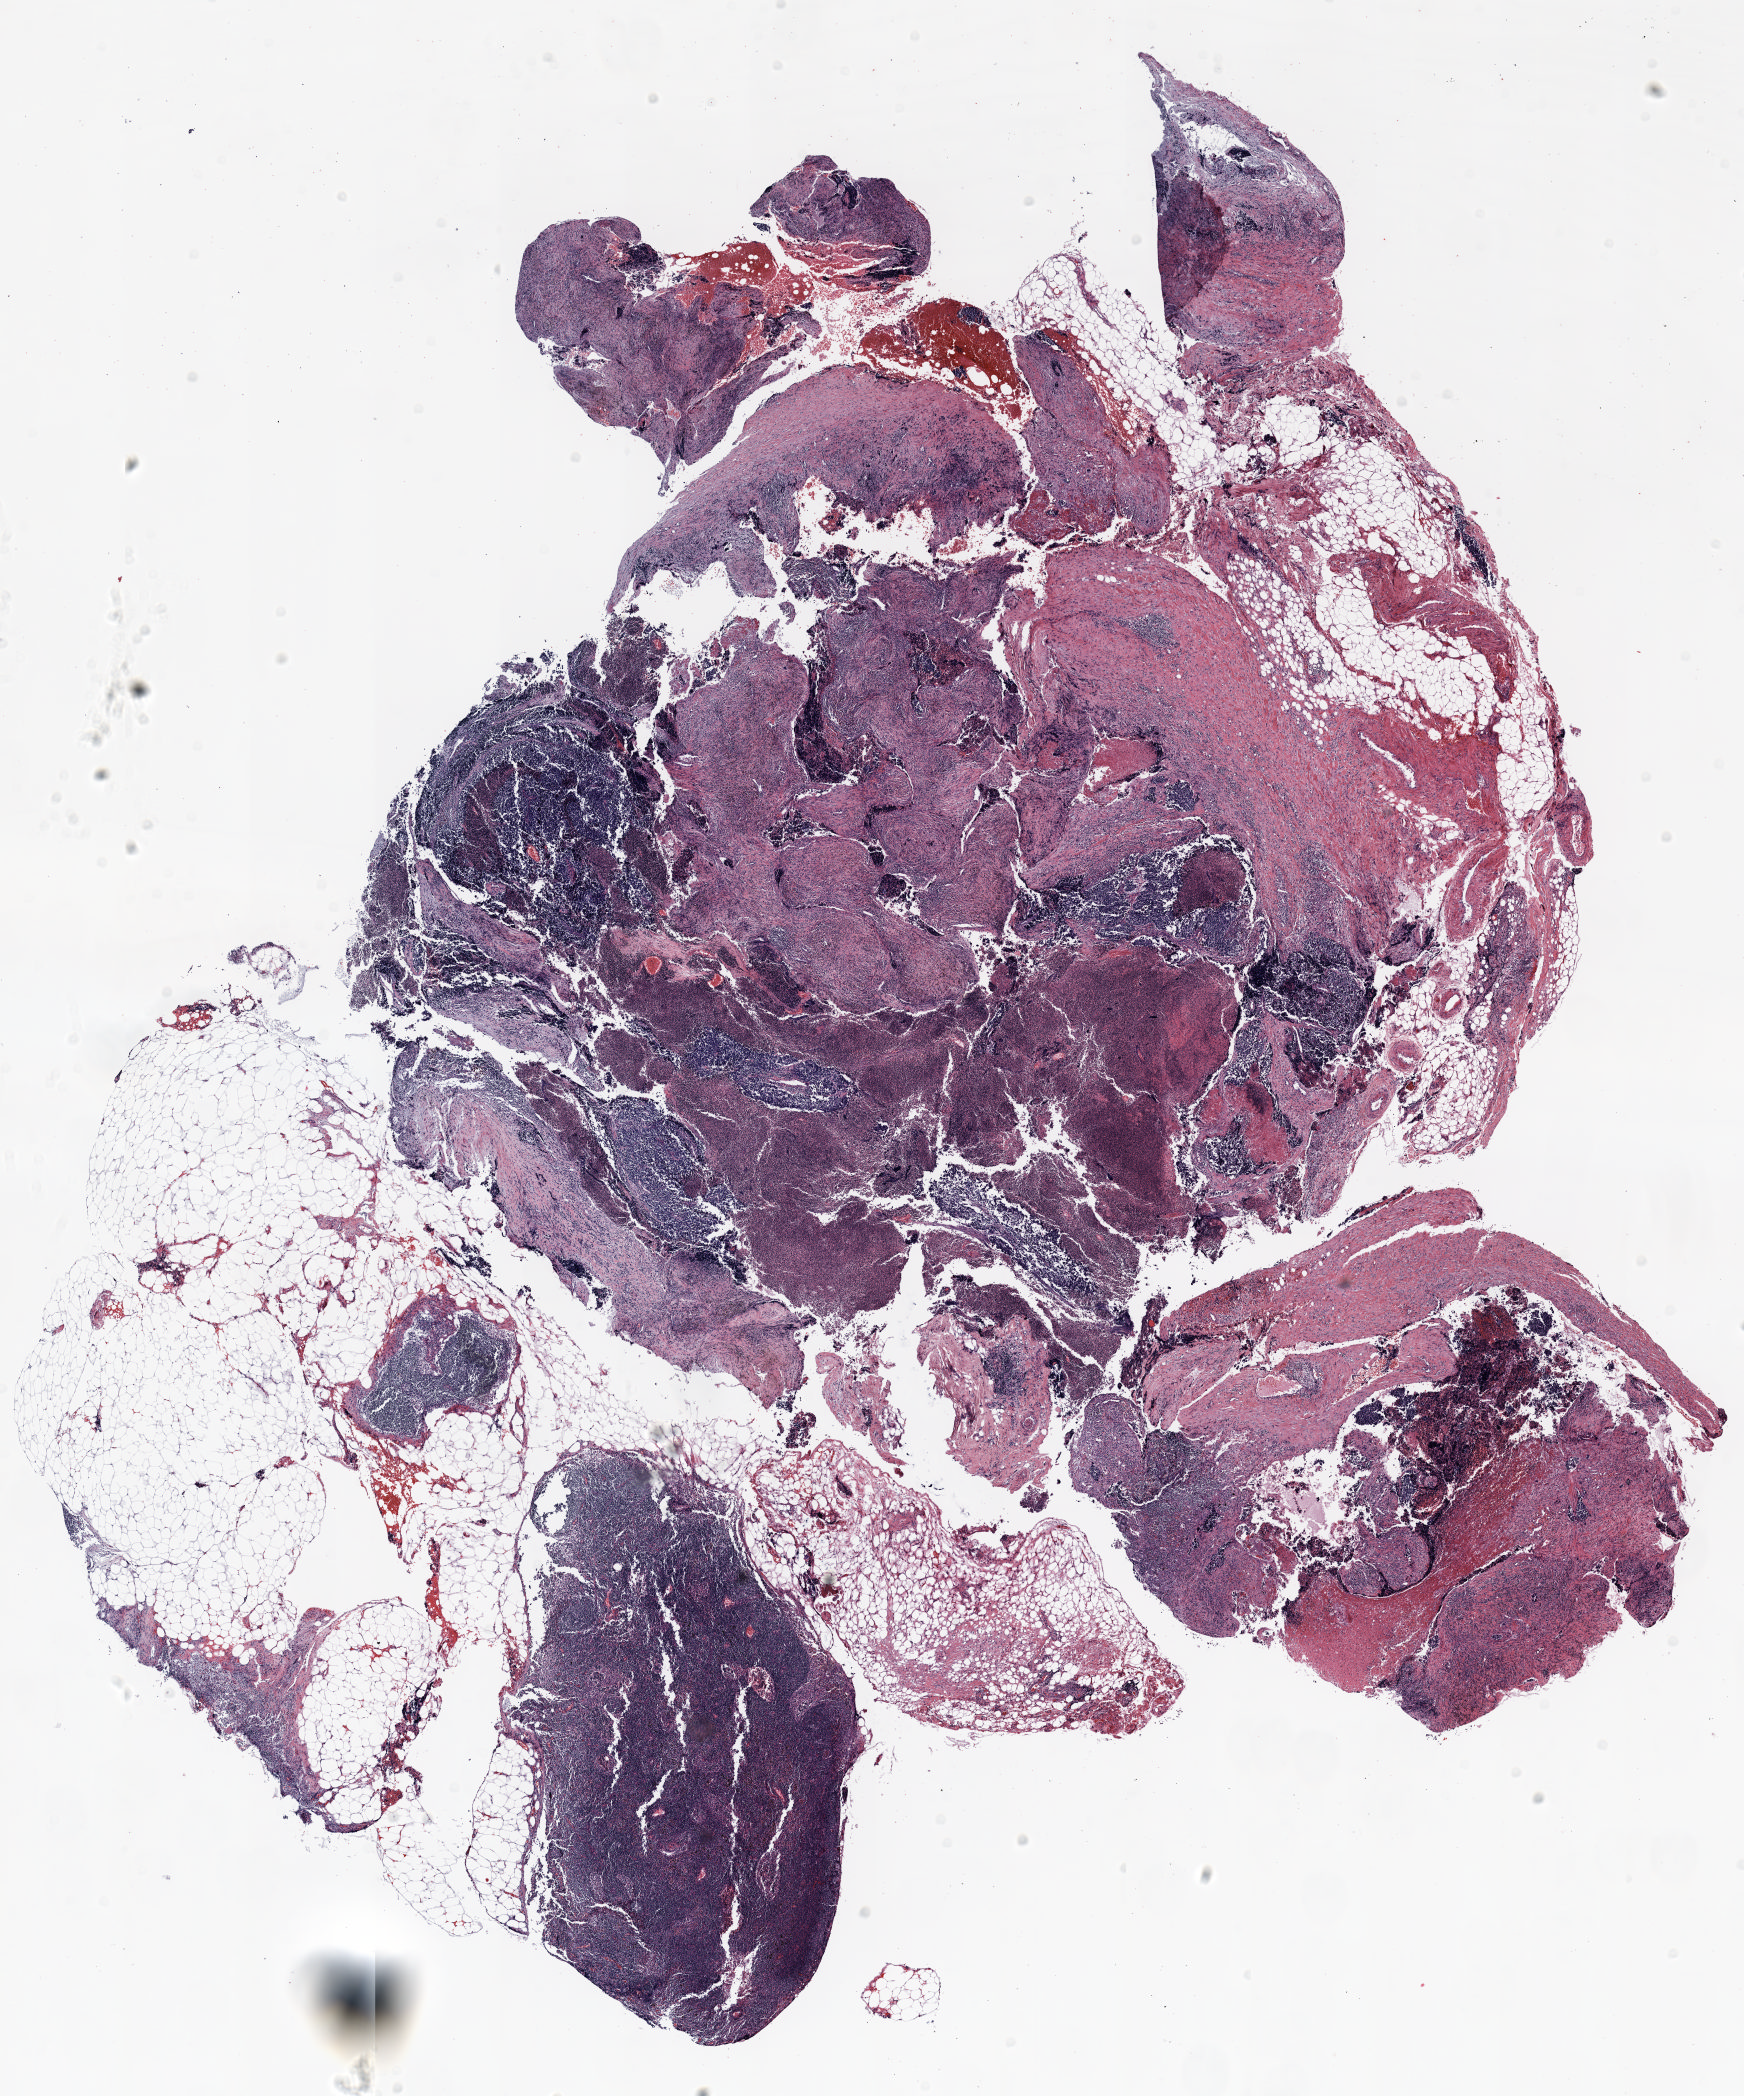
H&E-stained whole-slide image — whole scanned area (about 14.0 x 16.8 mm, acquisition: 20x scan) shown as a low-resolution overview. FFPE section. Lung. Male, age 68 at enrolment. Current smoker at enrolment.
Participant's lung-cancer diagnosis: Small cell carcinoma, NOS (ICD-O-3 8041/3).